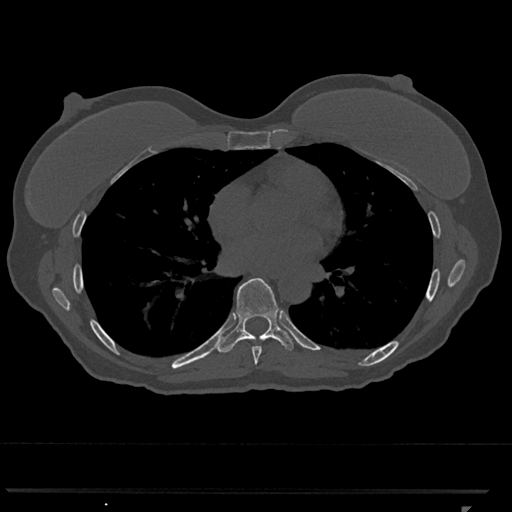
CT including the spine, one axial slice; position 680 of 793 along the scan axis; bone window (W 1800 / L 400 HU); 0.5 mm slice thickness; 512 × 512 image matrix, field of view 380 × 380 mm. Female patient, age 62 years. Case-level facts recorded for this patient, not image findings: primary cancer: renal.
Structures marked on this image (semi-automatically segmented with operator editing):
- T7 vertebra: bounding box (x1, y1, x2, y2) in pixels: (252, 346, 262, 365)
- T8 vertebra: (217, 278, 295, 353)